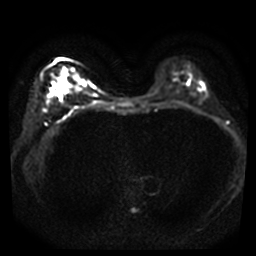
Breast MRI, one axial slice; position 17 of 40 along the scan axis; diffusion-weighted series; image 2 of 4 stored at this slice position (different b-values; order by instance number); 3 T; 5 mm slice thickness; 256 × 256 image matrix, field of view 320 × 320 mm. Female patient.
Structures marked on this image (outlined manually by an expert reader):
- tumour on diffusion-weighted imaging: bounding box <56,75,68,95> (left, top, right, bottom; pixels)